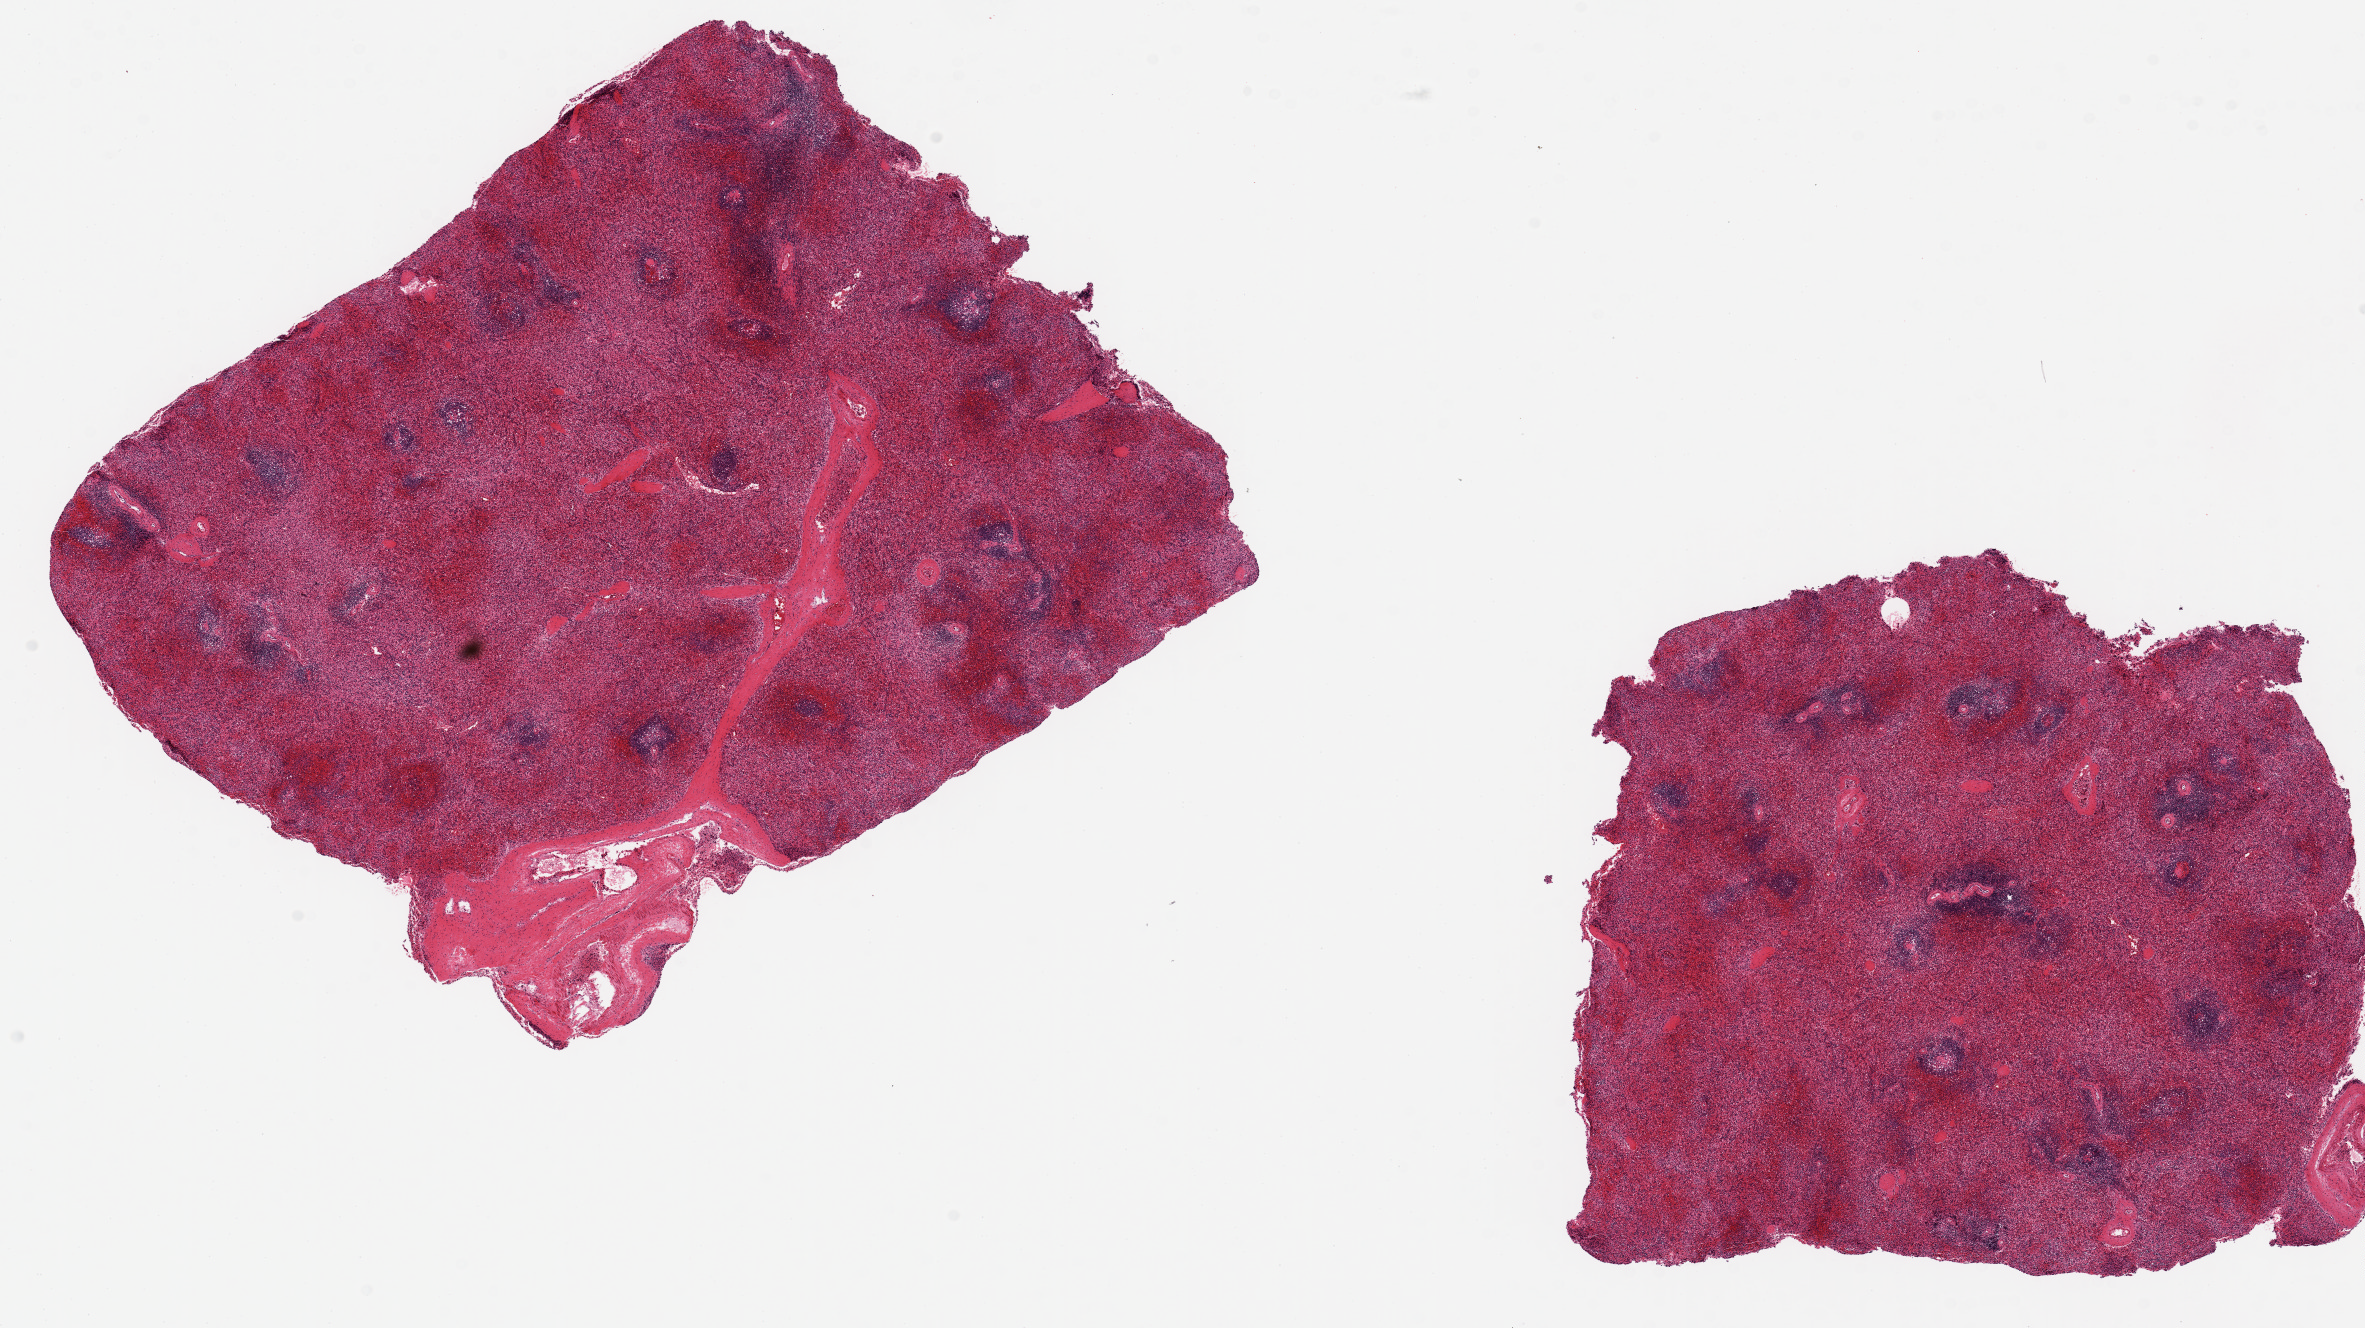
Digitized H&E-stained section, whole scanned area (about 18.7 x 10.5 mm) shown as a low-resolution overview, PAXgene-fixed, paraffin-embedded tissue, sampled site (target tissue): spleen, tissue donor sample. Donor: male.
Review note (as recorded): 2 pieces ~7x6mm. Congested, badly autolyzed.